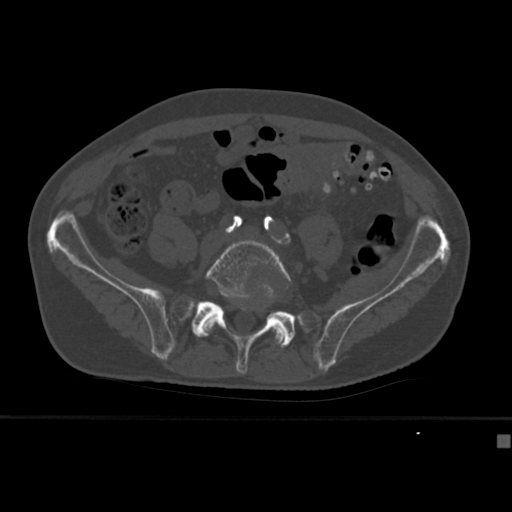
CT including the spine, one axial slice. Slice 80 of 430 in the series (ordered by position). 120 kVp. Bone window (W 1800 / L 400 HU). 512 × 512 image matrix. Male patient, age 64 years. Case-level facts recorded for this patient, not image findings: primary cancer: uterus.
Outlined on this slice (semi-automatic segmentation, software-assisted and operator-edited):
- L5 vertebra: box from (x=196, y=236) to (x=292, y=348) px